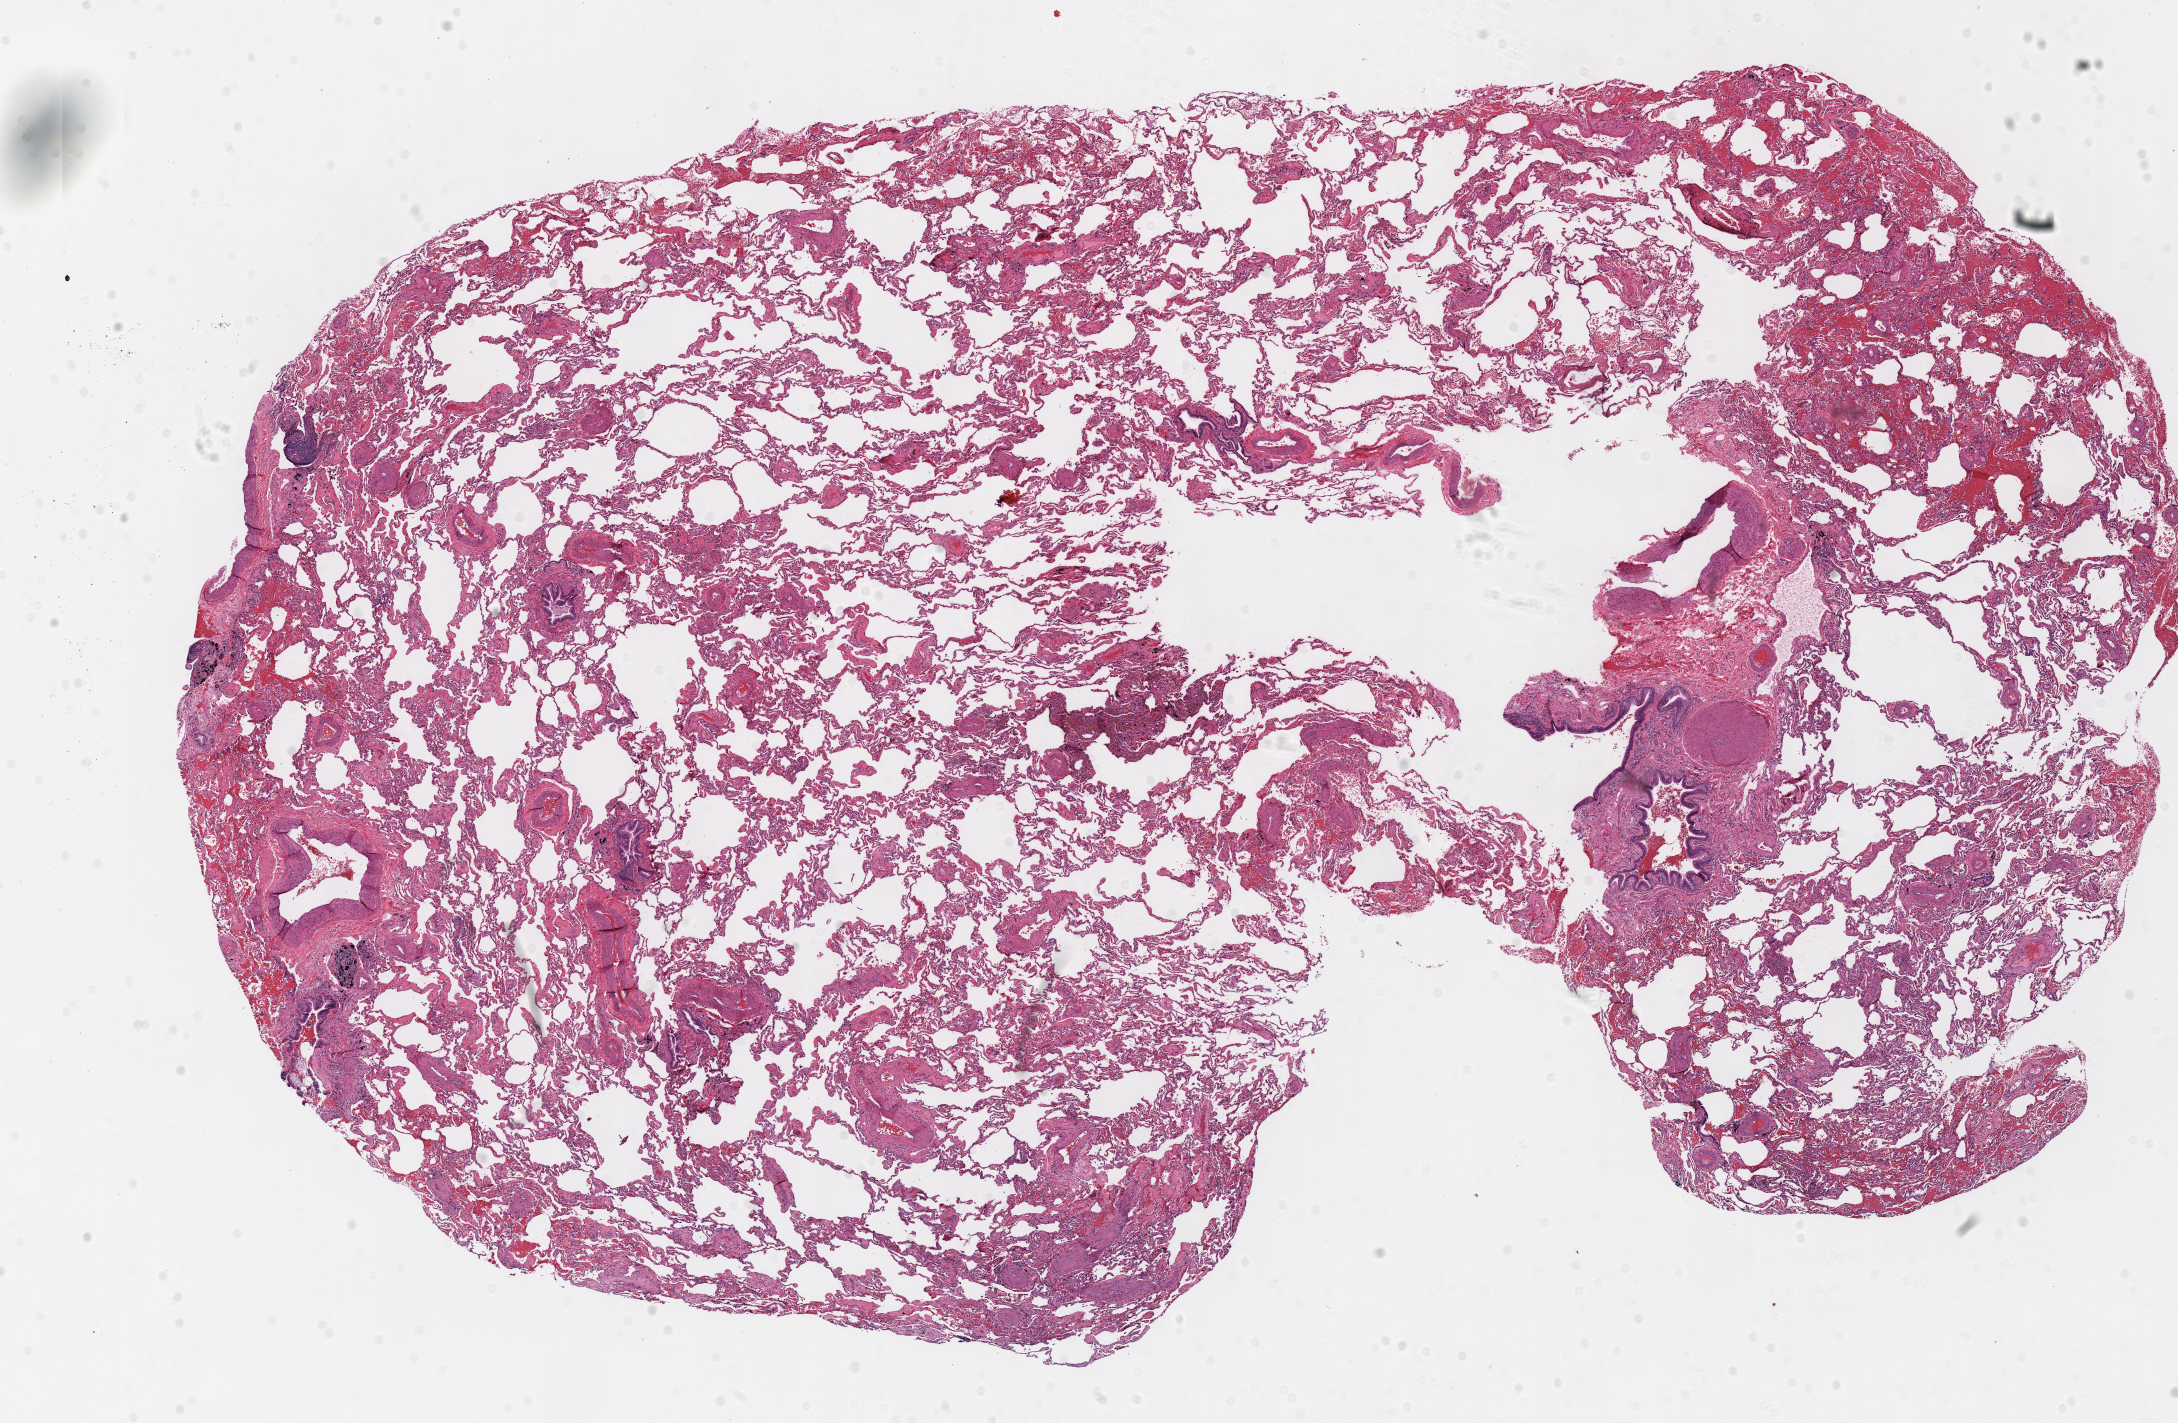
Digitized H&E tissue section (whole slide), whole scanned area (about 17.1 x 11.2 mm) shown as a low-resolution overview. Frozen section from the top of the tissue portion. Lung, solid tissue normal (non-tumour tissue) sample. Male patient; age at initial diagnosis 71 years.
This section: solid tissue normal (non-tumour) sample from the same patient. Patient diagnosis: Squamous cell carcinoma, NOS (lower lobe, lung).